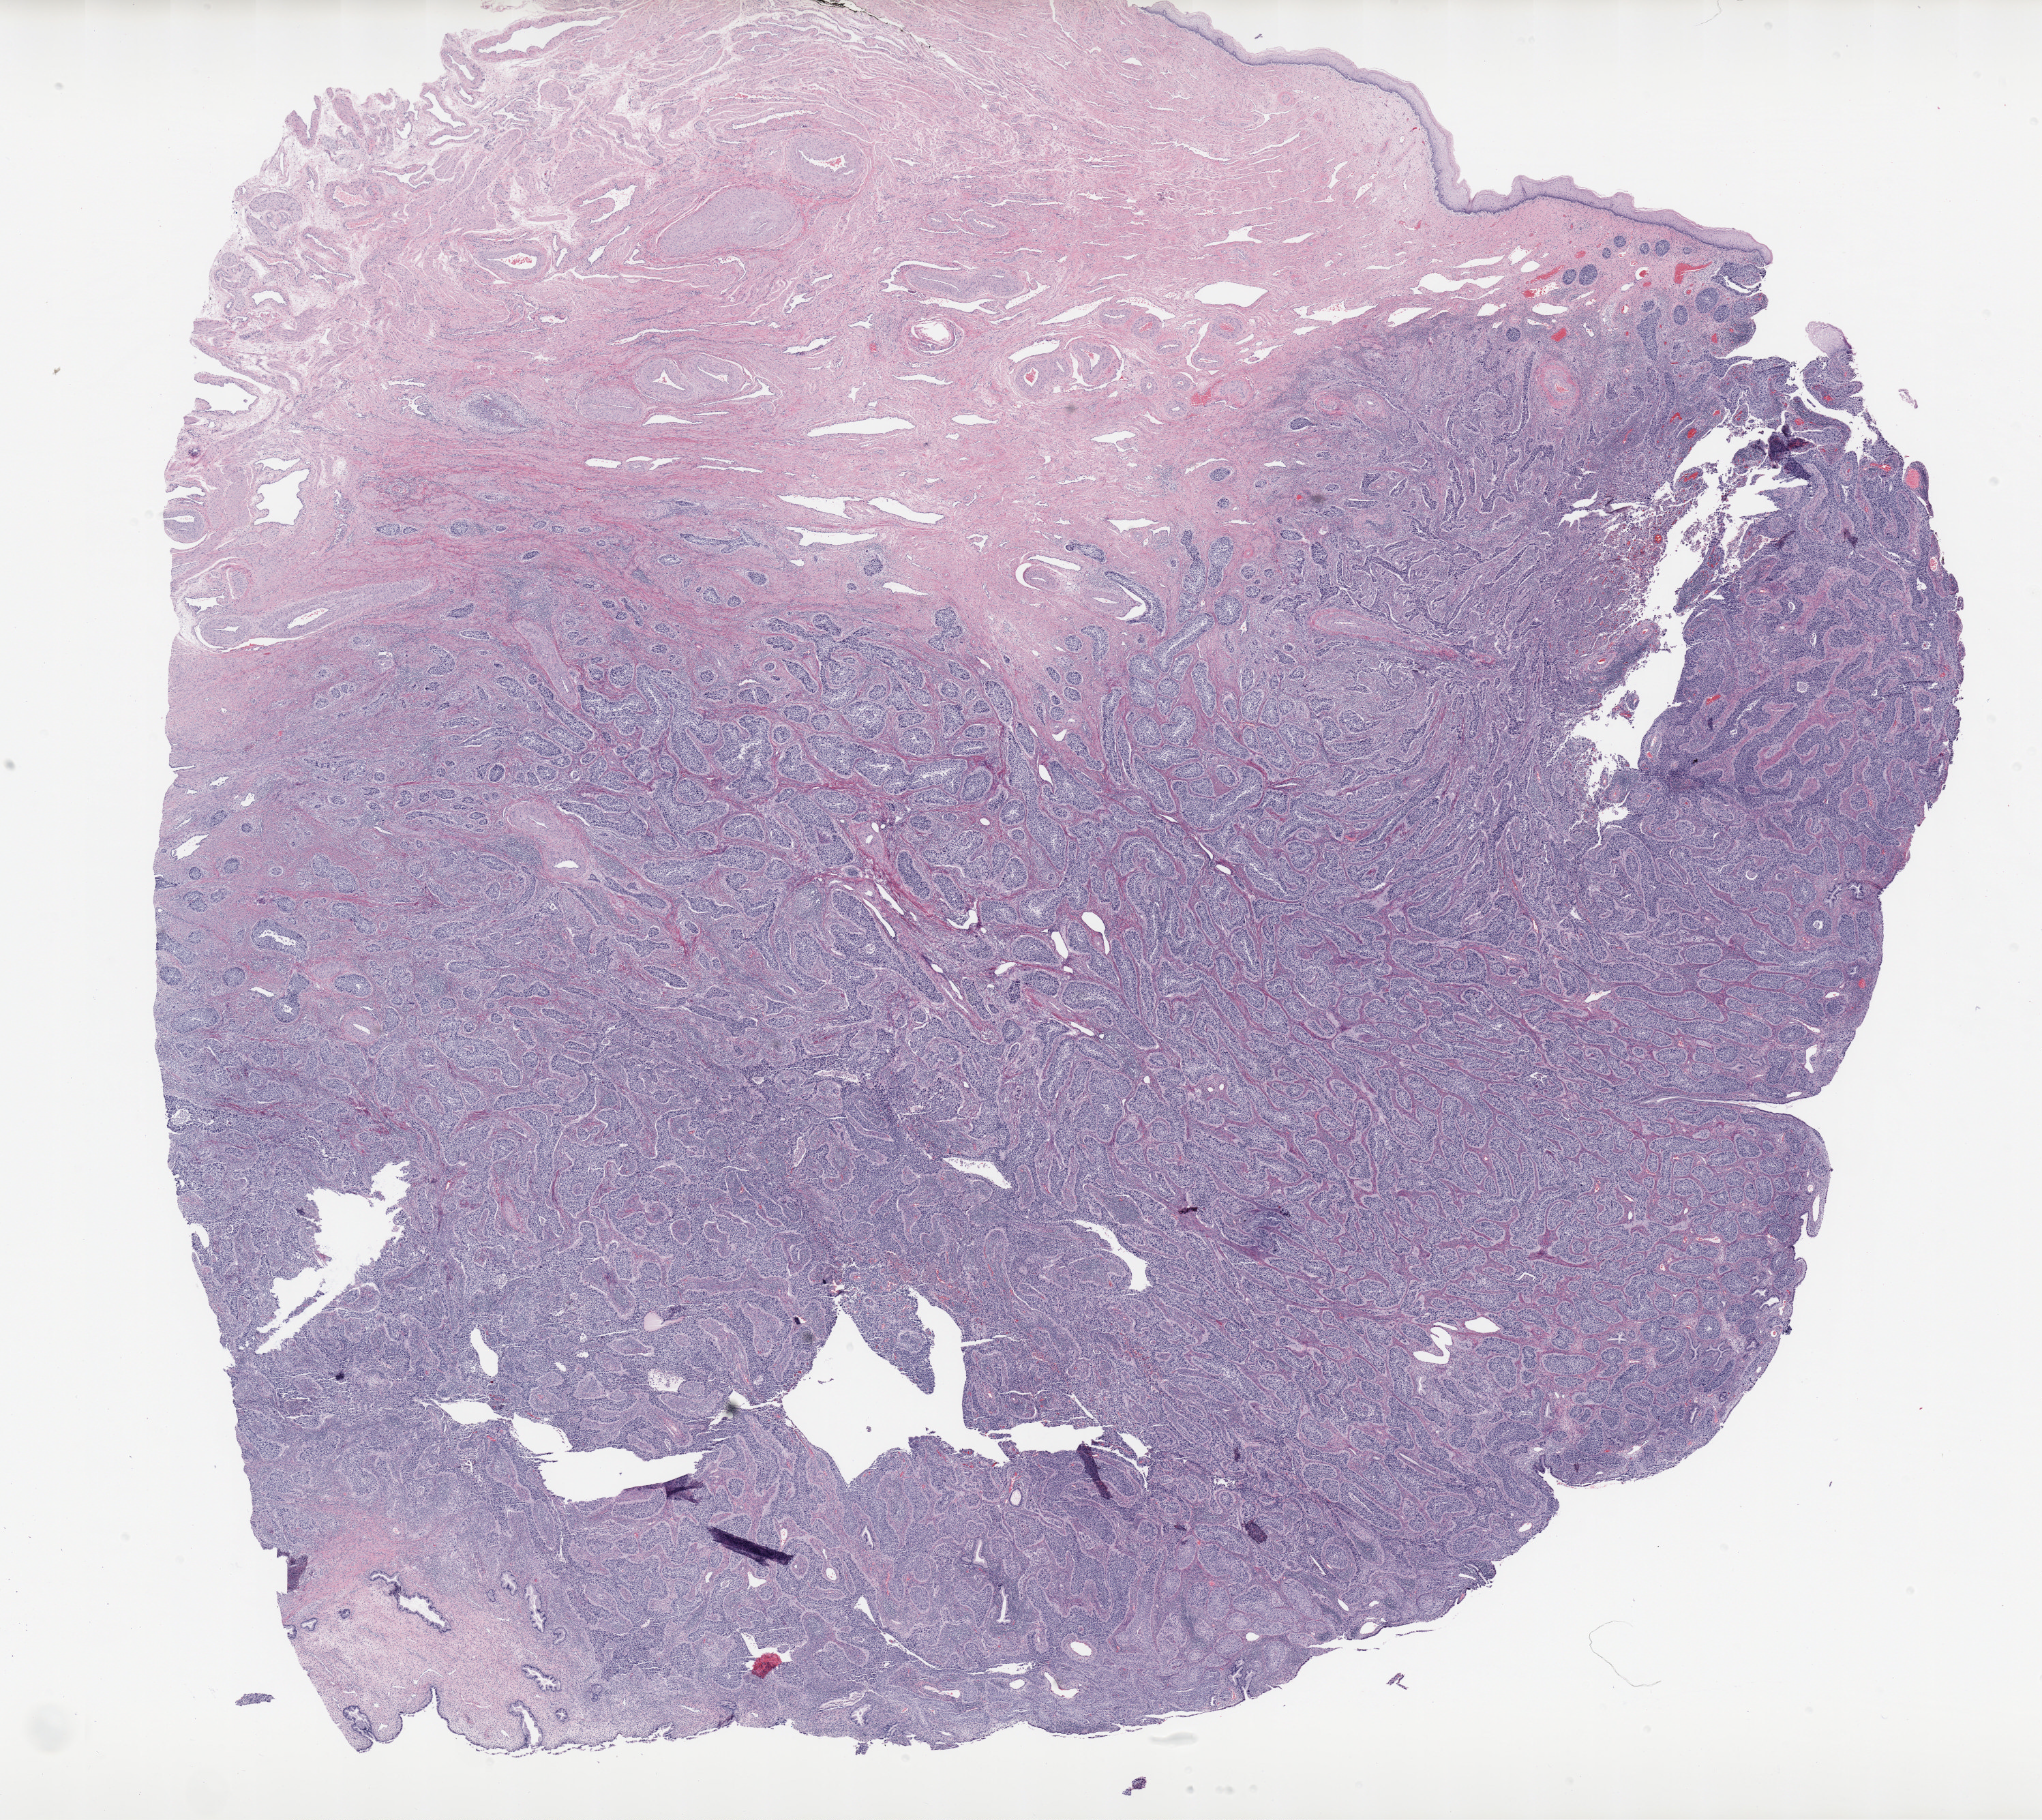
Digitized H&E tissue section (whole slide) — shown as a low-resolution overview of the whole scanned area (about 23.9 x 21.3 mm, slide scanned at 20x). Formalin-fixed paraffin-embedded (FFPE) diagnostic section. Cervix, primary tumour sample. Female, age 40 years at initial diagnosis. Histologic grade: G3 (poorly differentiated).
Pathologic diagnosis: Squamous cell carcinoma, NOS (cervix uteri). Lymph nodes positive (case pathology): 0 of 48 examined. FIGO stage: IB1.